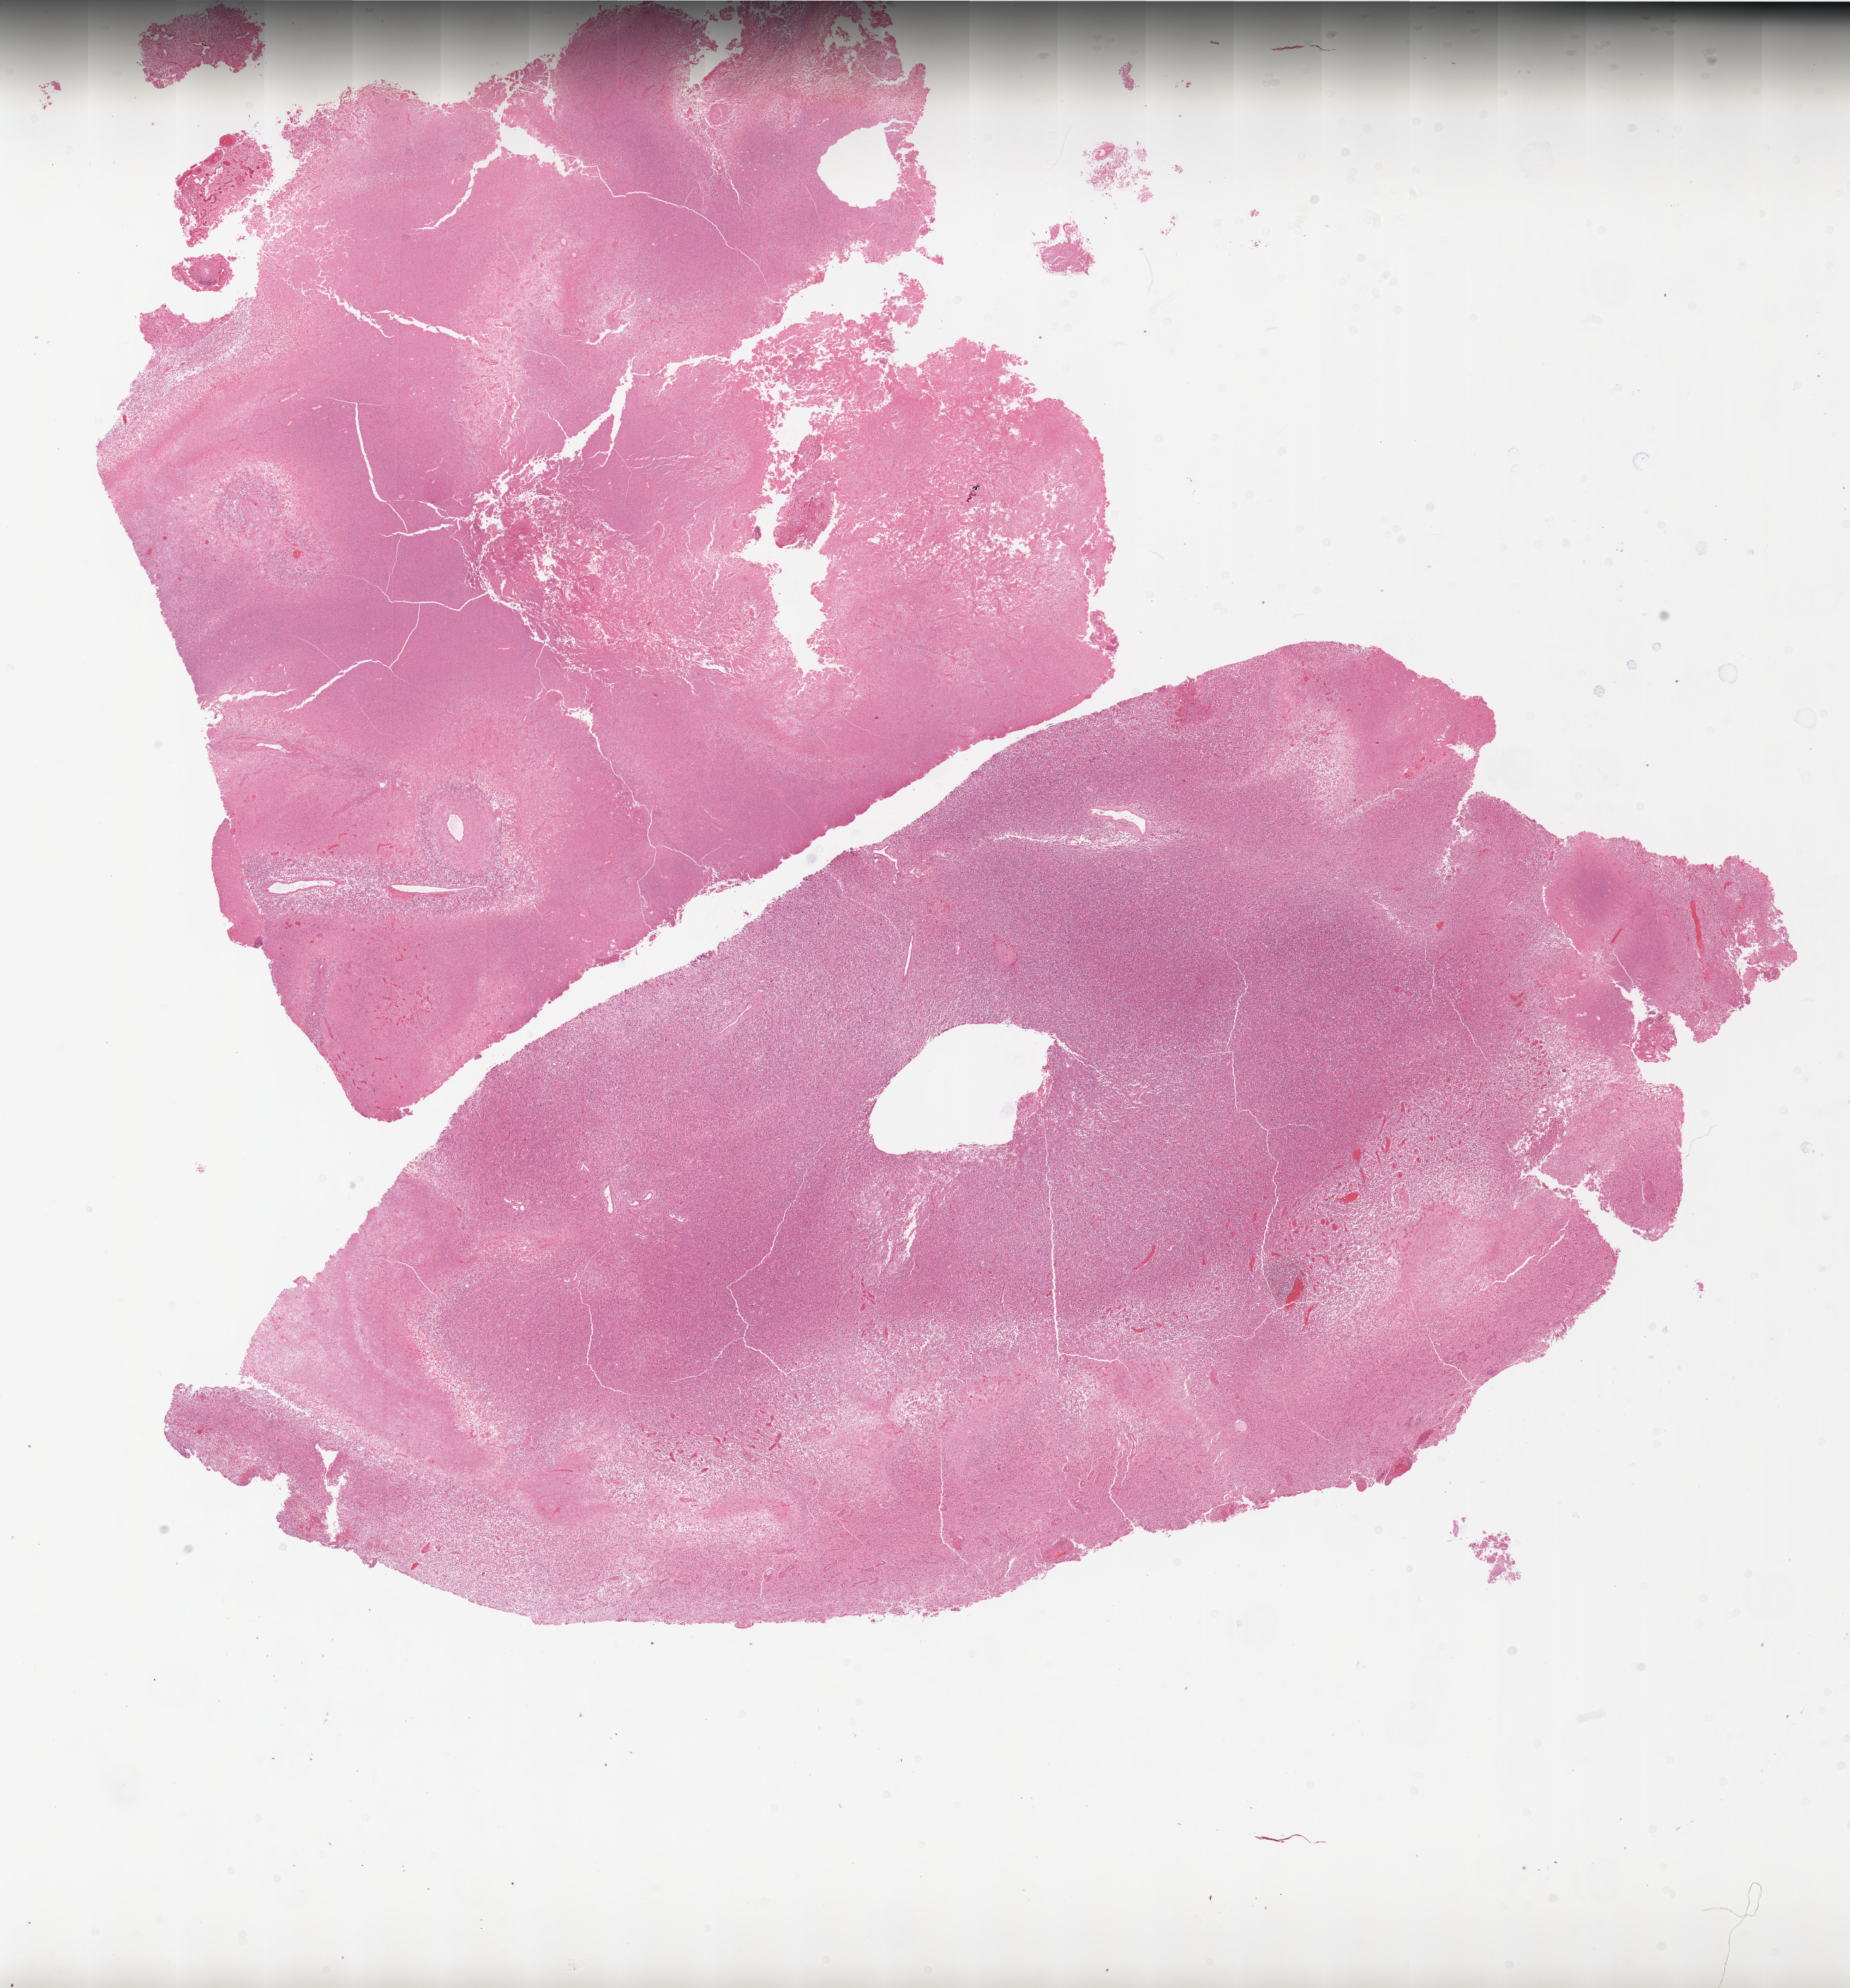
Whole-slide histology image, Hematoxylin and eosin (H&E) stained — shown as a low-resolution overview of the whole scanned area (about 21.0 x 22.5 mm), formalin-fixed paraffin-embedded (FFPE) diagnostic section, sample: primary tumour, brain. Male, age 68 years at initial diagnosis.
Histologic diagnosis: Glioblastoma.